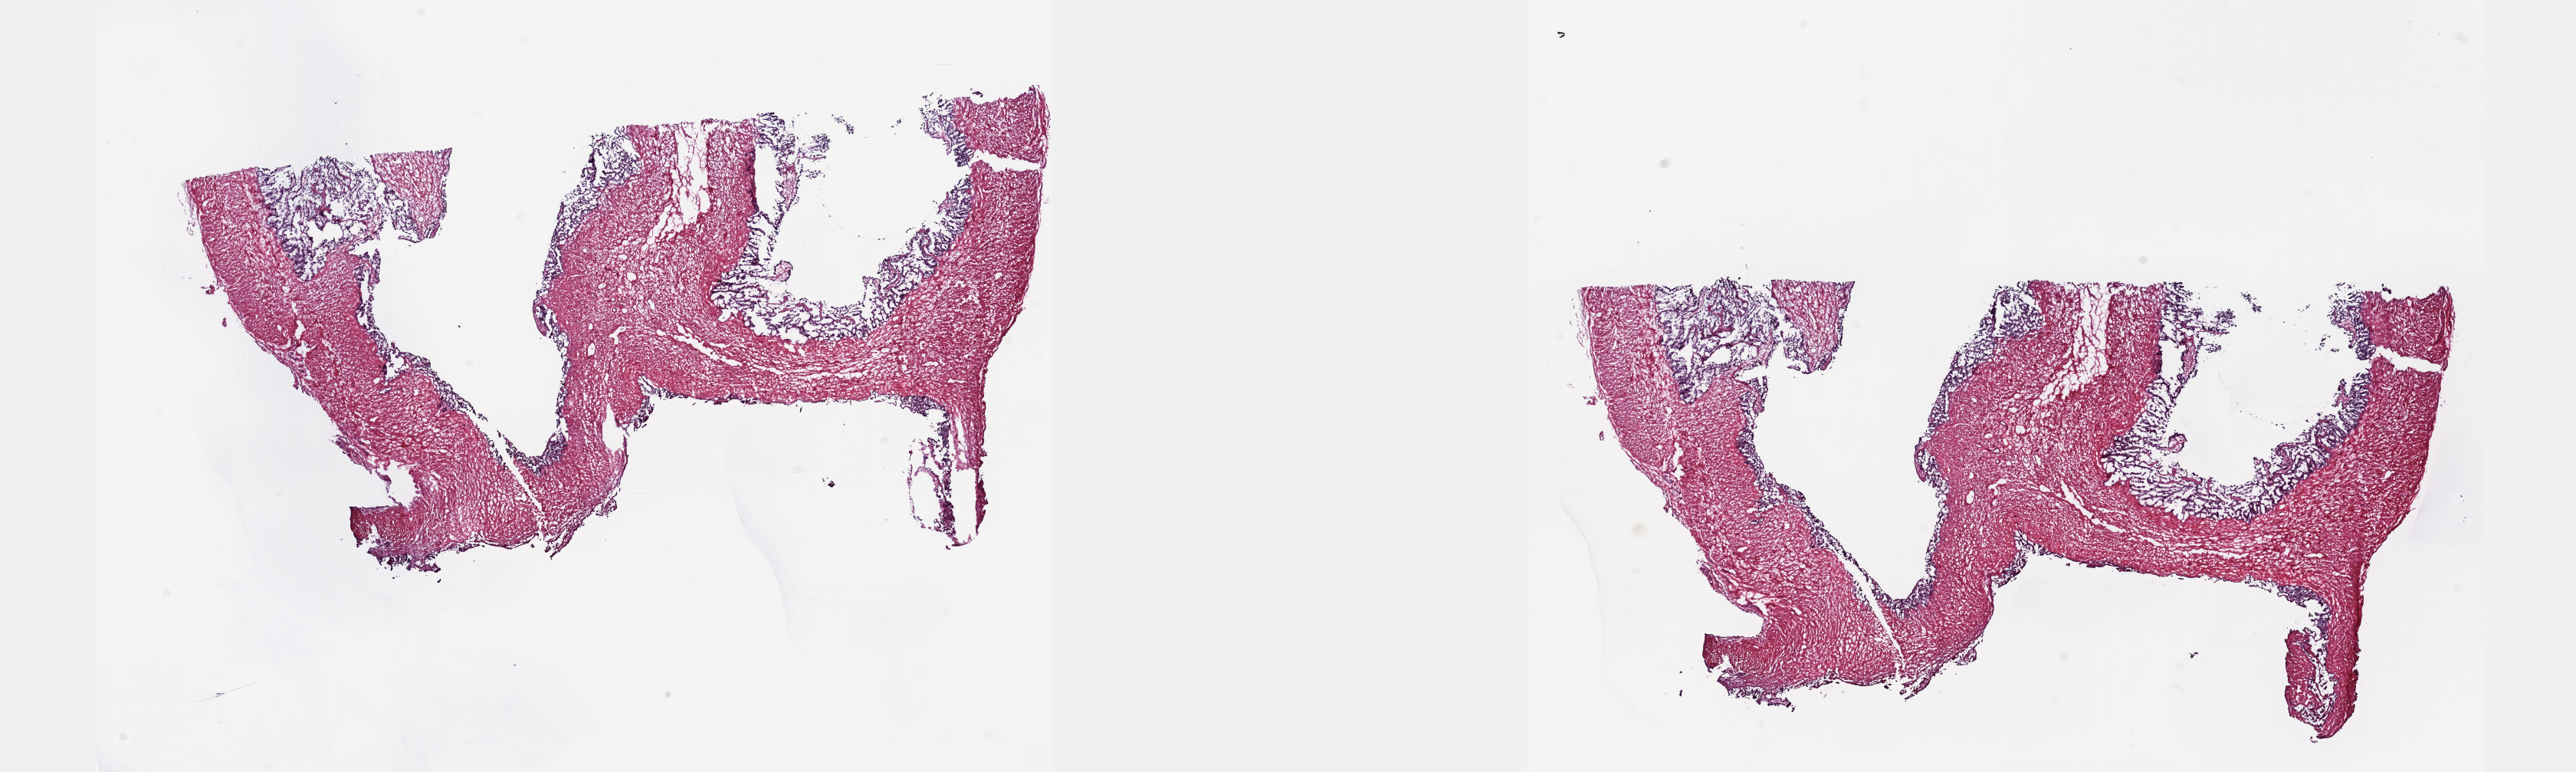
Hematoxylin and eosin (H&E) stained whole-slide image, shown as a low-resolution overview of the whole scanned area (about 27.1 x 8.1 mm, acquisition: 20x scan), frozen section from the top of the tissue portion, solid tissue normal (non-tumour tissue) sample from the prostate. Male, age 55 years at initial diagnosis. Pathologist review of this section (percent, as recorded): tumour cells 0%, tumour nuclei 0%, normal cells 40%, stromal cells 60%, necrosis 0%. Infiltration values recorded for this section: lymphocyte infiltration 40%, monocyte infiltration 20%, neutrophil infiltration 20%.
This section: solid tissue normal (non-tumour) sample from the same patient. Patient diagnosis: Adenocarcinoma, NOS.